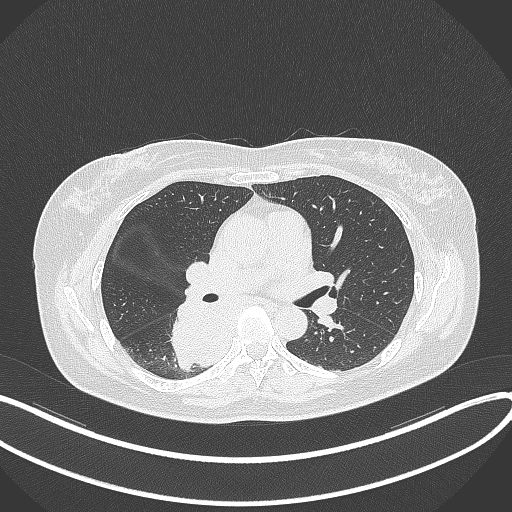
Chest CT, one axial slice. Position 205 of 331 along the scan axis. Reconstruction kernel B70f. Lung window (W 1500 / L -600 HU). 1 mm slice thickness. 512 × 512 image matrix. Patient: female, 54 years. Case-level facts recorded for this patient, not image findings: clinical TNM (as recorded): T4 N0 M0.
Annotated regions visible in this slice (bounding box drawn by a radiologist):
- lung tumour (recorded histology: adenocarcinoma): box from (x=167, y=295) to (x=223, y=370) px